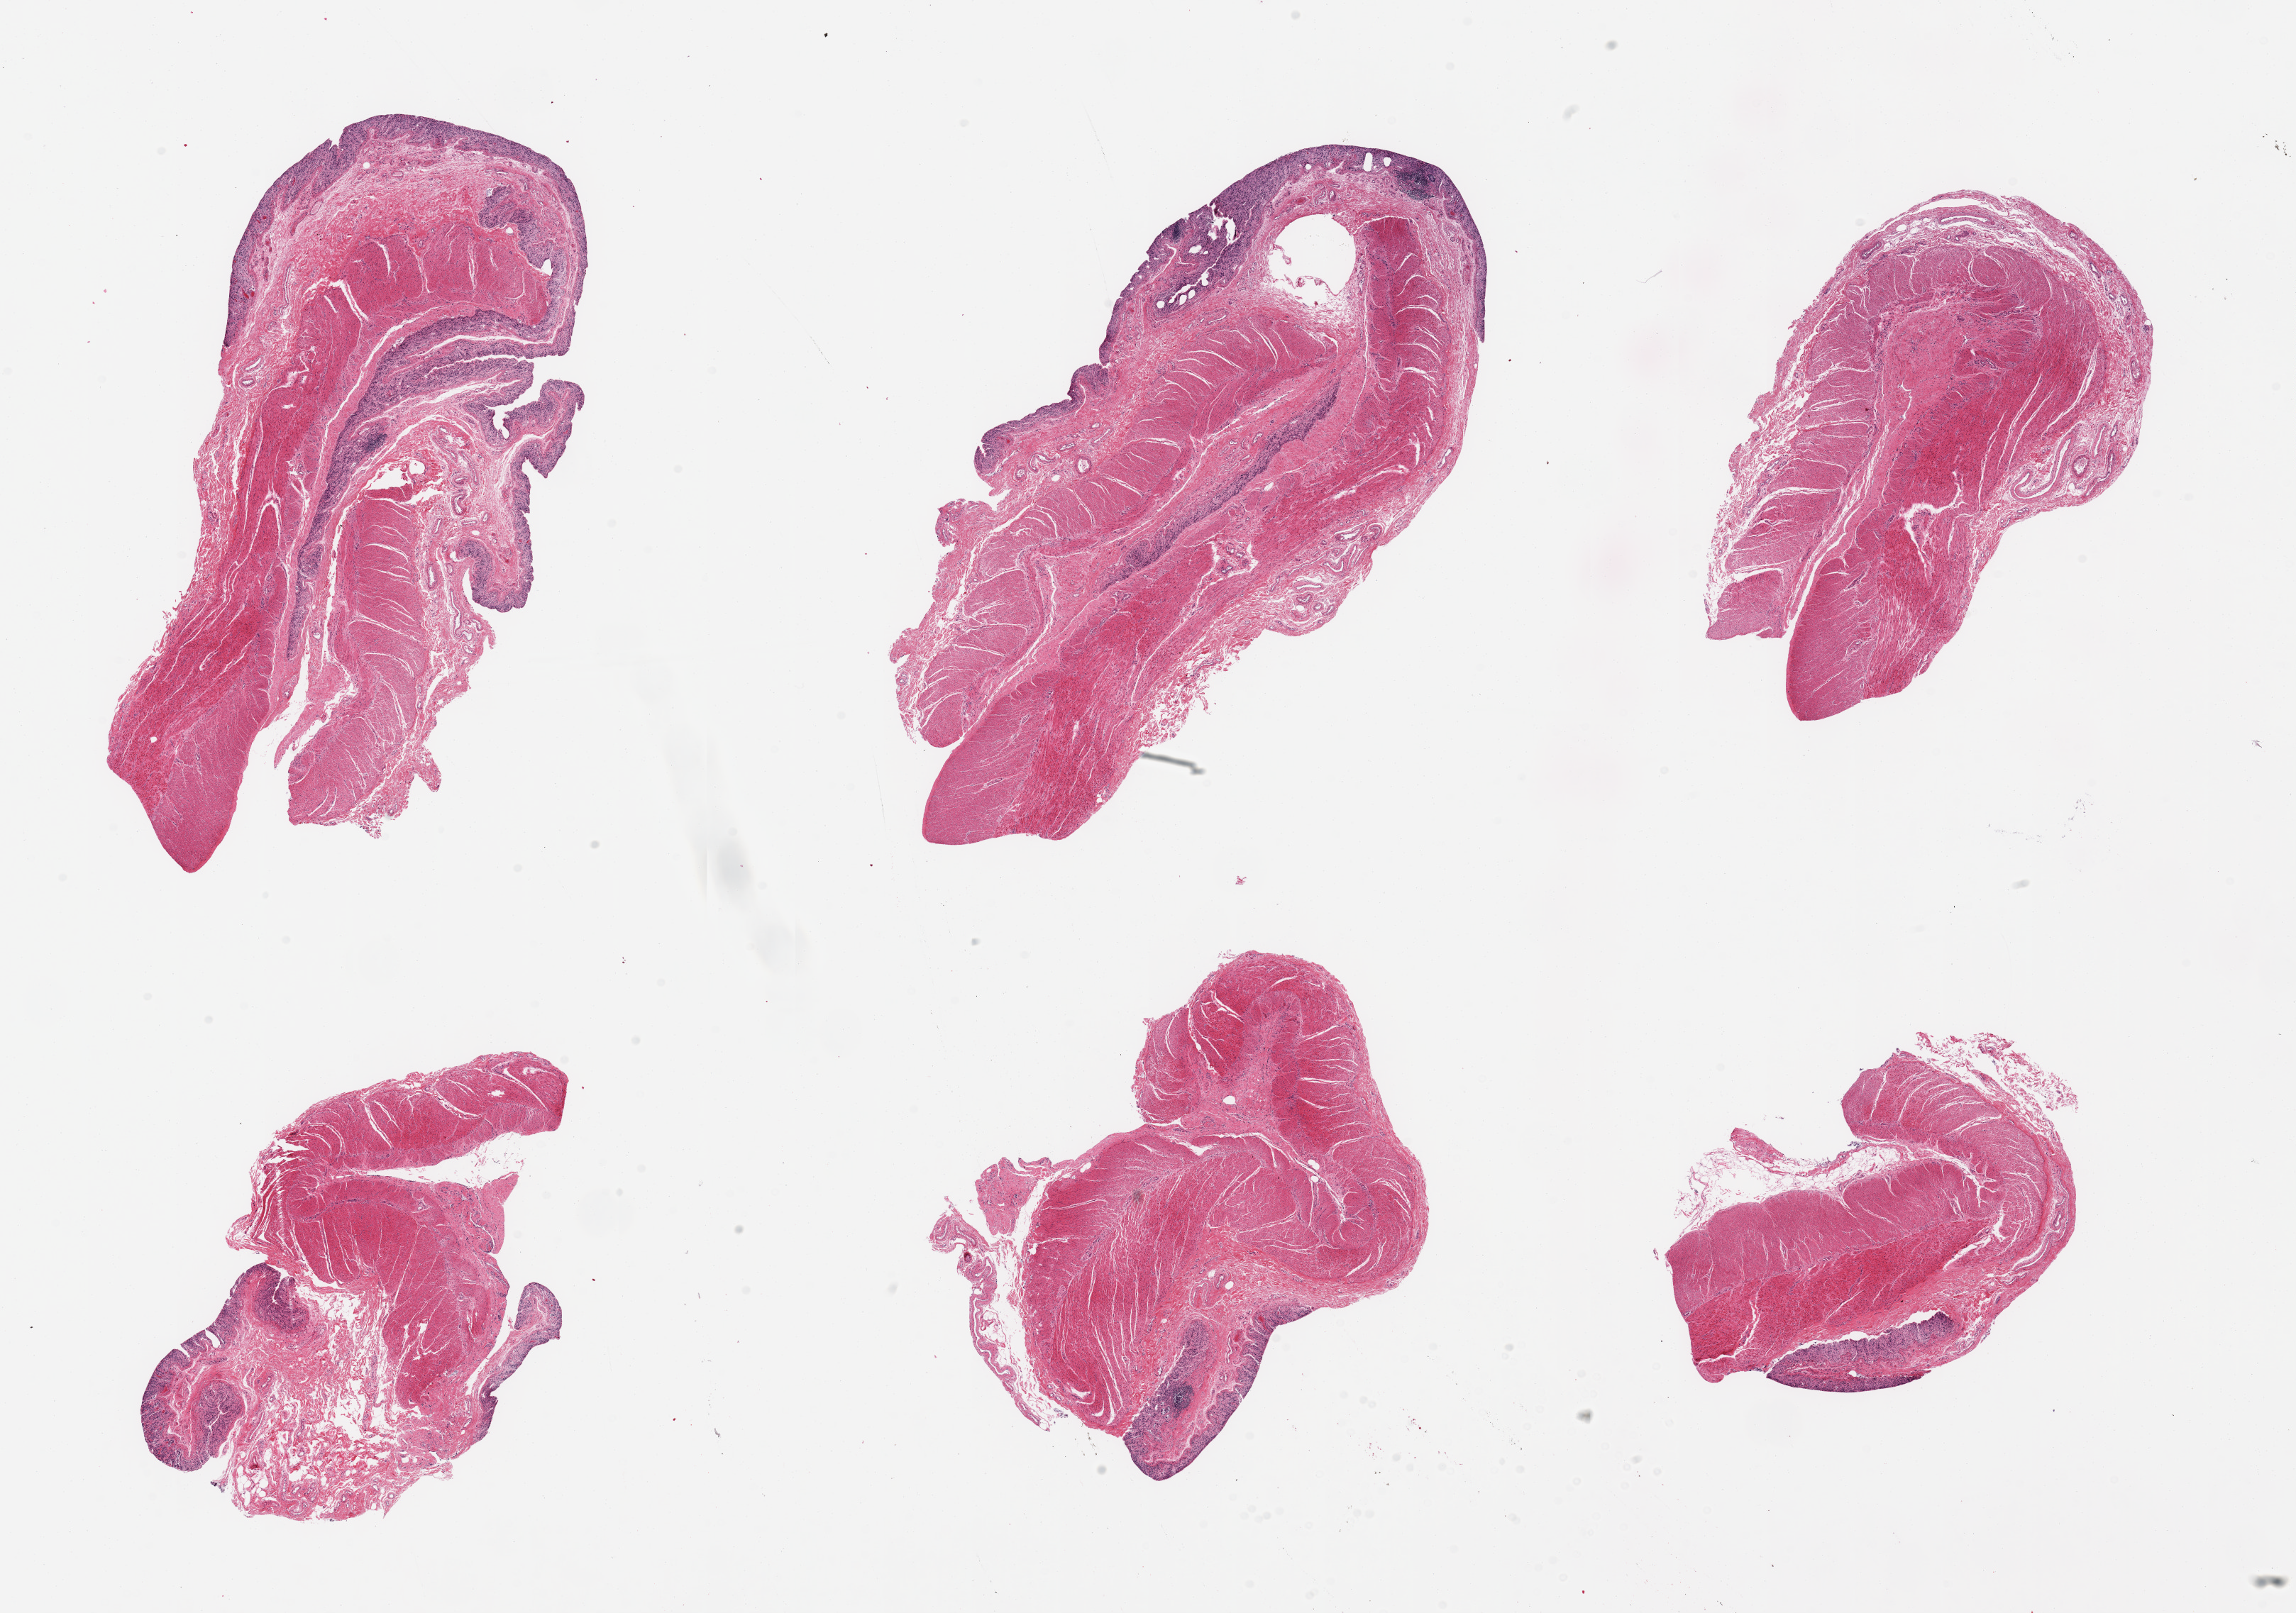
Digitized haematoxylin and eosin-stained section, brightfield — whole scanned area (about 25.6 x 18.0 mm, acquisition: 20x scan) shown as a low-resolution overview, PAXgene-fixed, paraffin-embedded tissue, sampled site (target tissue): transverse colon, tissue donor sample. Male donor.
Review note (as recorded): 6 pieces, mucosa up to ~0.3mm, largely sloughed.